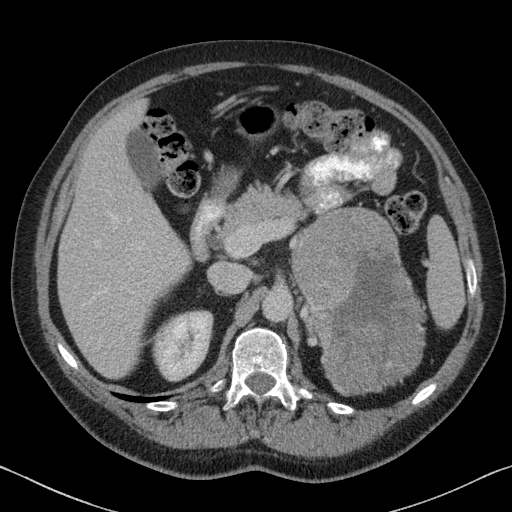
Contrast-enhanced abdominal CT, one axial slice. Slice 48 of 88 in the series (ordered by position). Reconstruction kernel B31f. 120 kVp. Soft-tissue window (W 400 / L 40 HU). 3 mm slice thickness. 512 × 512 image matrix, field of view 366 × 366 mm. Patient: male, 51 years. Case-level facts recorded for this patient, not image findings: diagnosis: adrenocortical carcinoma; tumour side: left adrenal; tumour size at pathology: 16.5 cm; Ki-67 index: 30 %; stage (as recorded): 2.
Annotated regions visible in this slice (semi-automatically segmented with operator editing):
- mass: box from (x=297, y=208) to (x=424, y=395) px